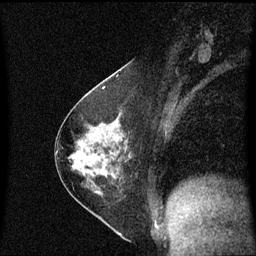
Breast MRI (dynamic contrast-enhanced), one sagittal slice. Slice 31 of 60 in the series (ordered by position). Dynamic contrast-enhanced series, image 2 of 3 at this slice position (ordered by acquisition). 1.5 T. TE 4.2 ms, TR 8.4 ms. 2 mm slice thickness. 256 × 256 image matrix, field of view 210 × 210 mm. Patient: female, 54 years. From the clinical record (not read from this slice): setting: breast cancer imaged before/during neoadjuvant chemotherapy; receptor status: HER2-positive.
Outlined on this slice (semi-automatically segmented with operator editing):
- analysis volume of interest (the breast-tissue region the enhancement analysis was run in; not a lesion): bounding box [x1, y1, x2, y2] px = [57, 118, 134, 190]
- tumour enhancement mask (voxels above the 70 % enhancement threshold inside the analysis volume of interest): [116, 138, 119, 141]